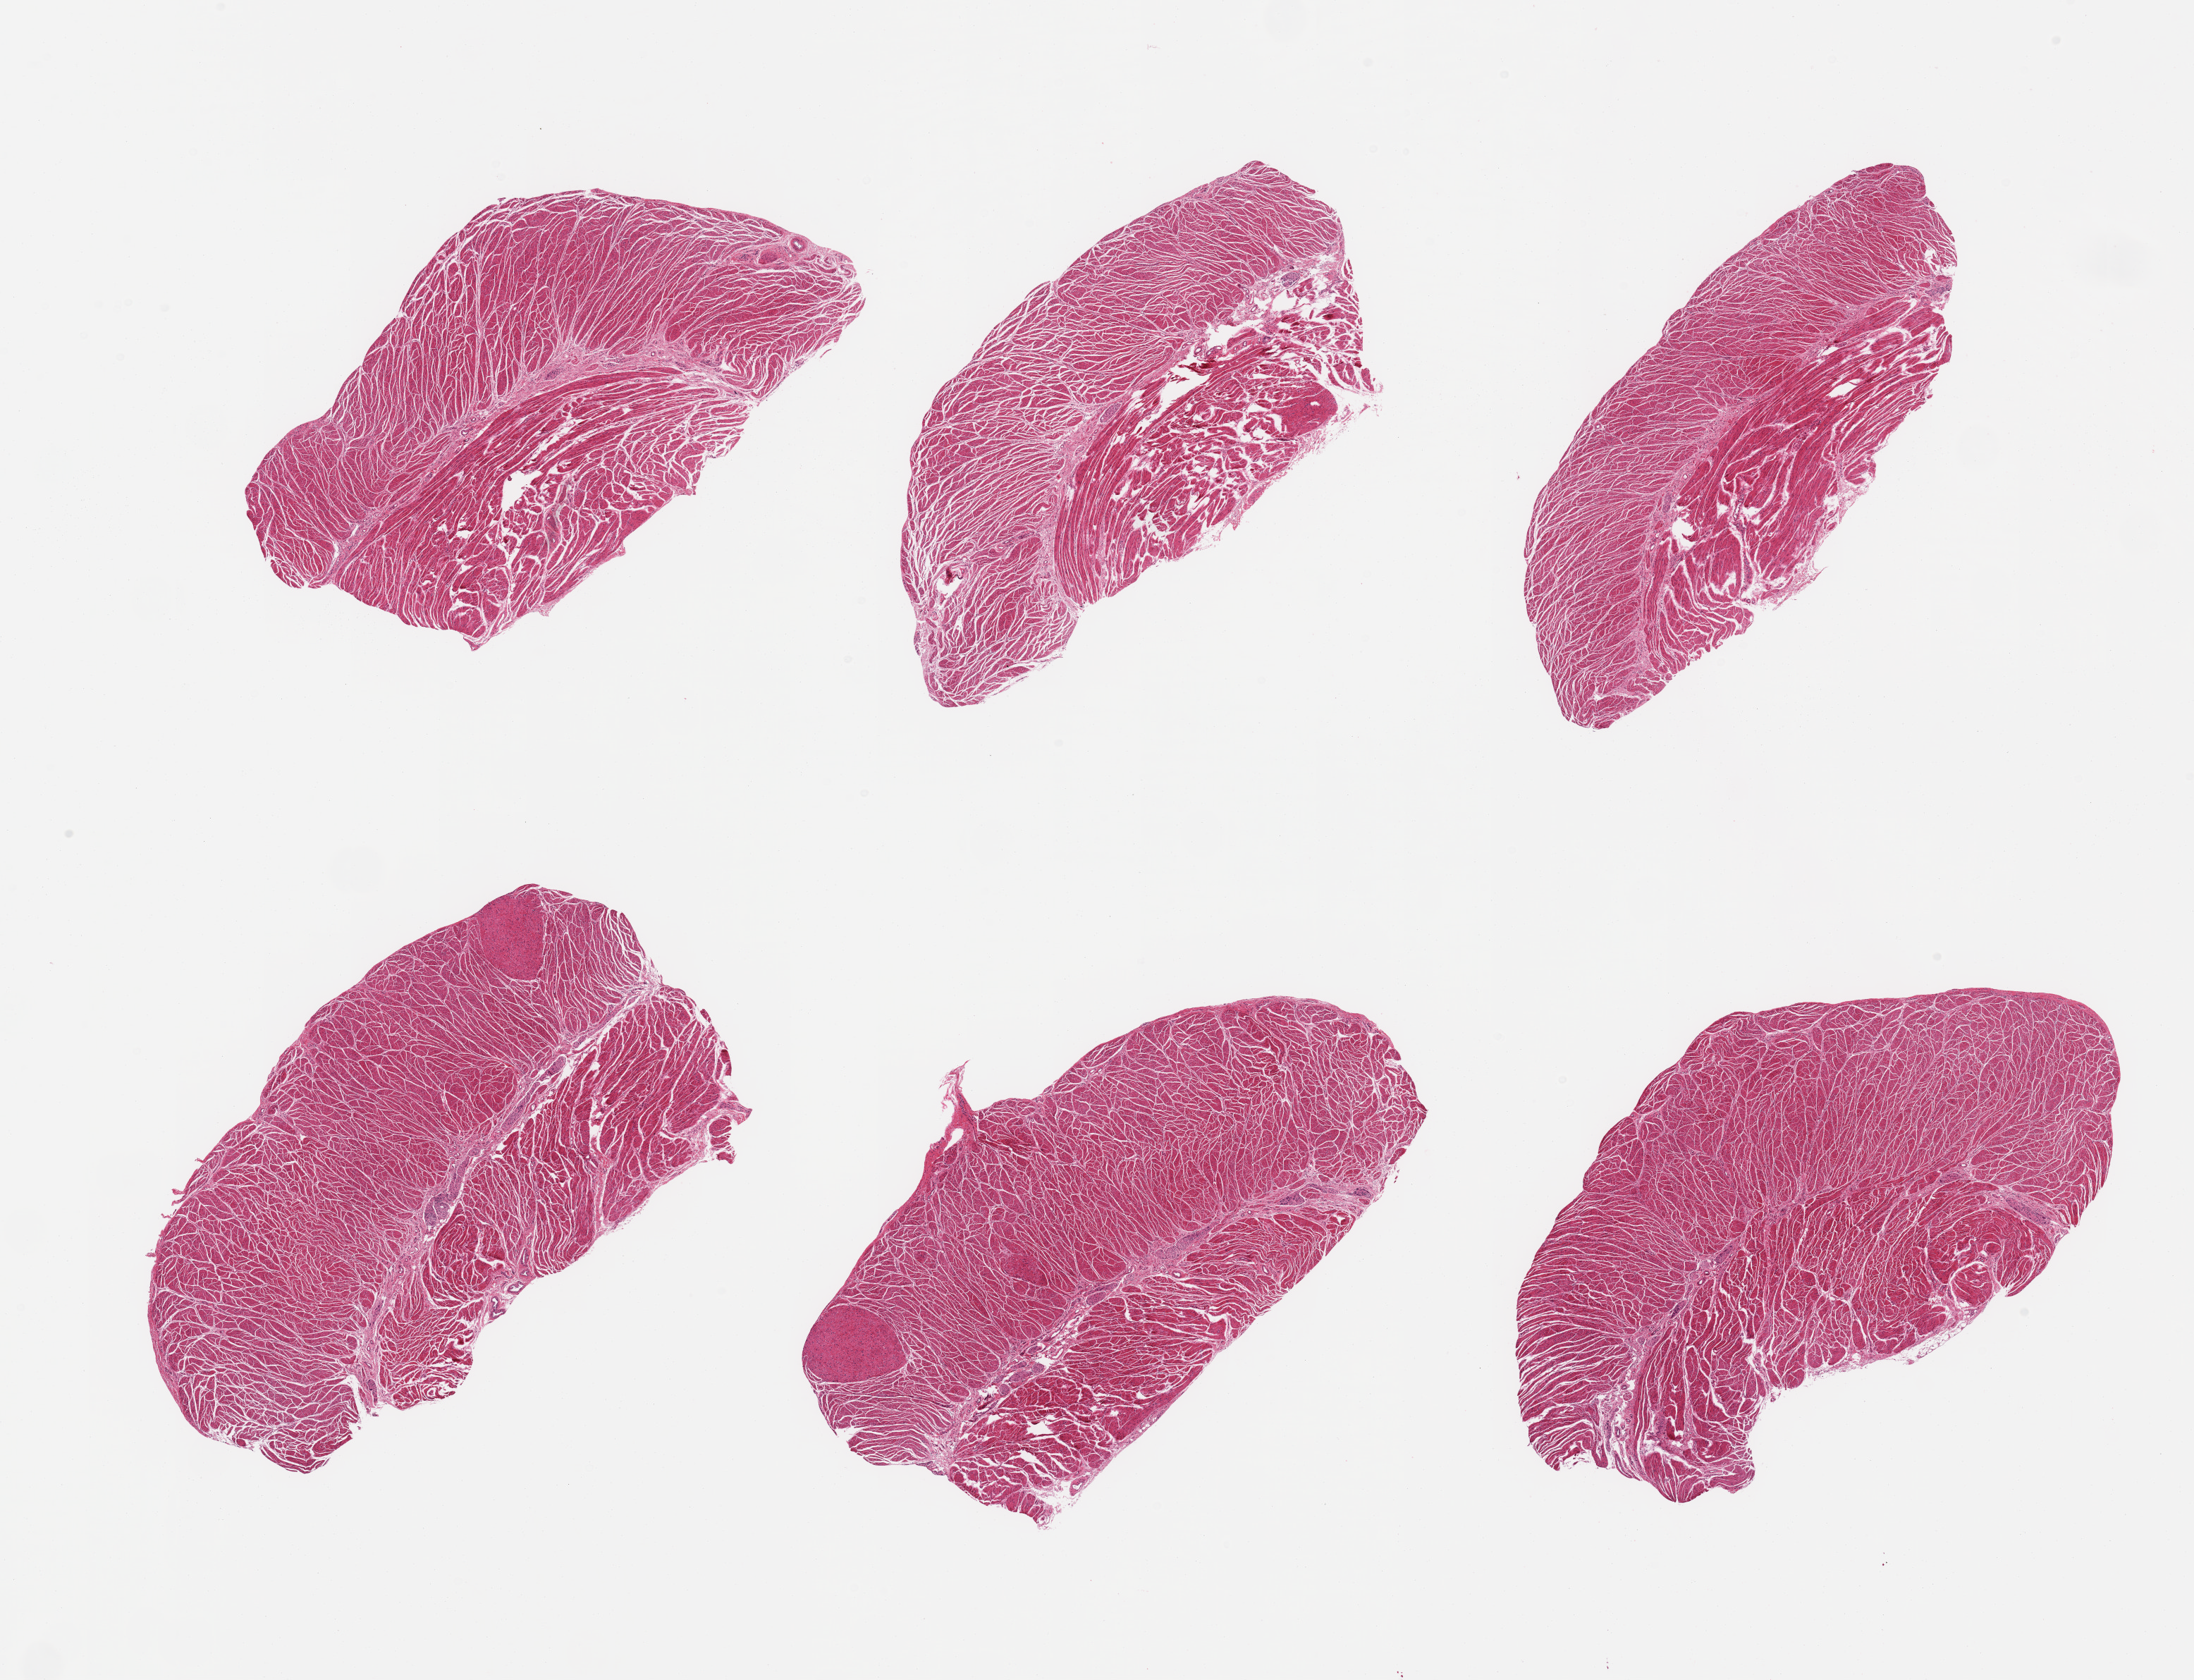
Whole-slide image, haematoxylin and eosin stain, brightfield, shown as a low-resolution overview of the whole scanned area (about 24.6 x 18.8 mm, from a 20x scan); PAXgene-fixed paraffin-embedded (PFPE) section; section of gastroesophageal junction (target tissue); donor tissue sample. Male donor.
Pathologist's review note for this sample: 6 pieces, confirmed target muscularis.